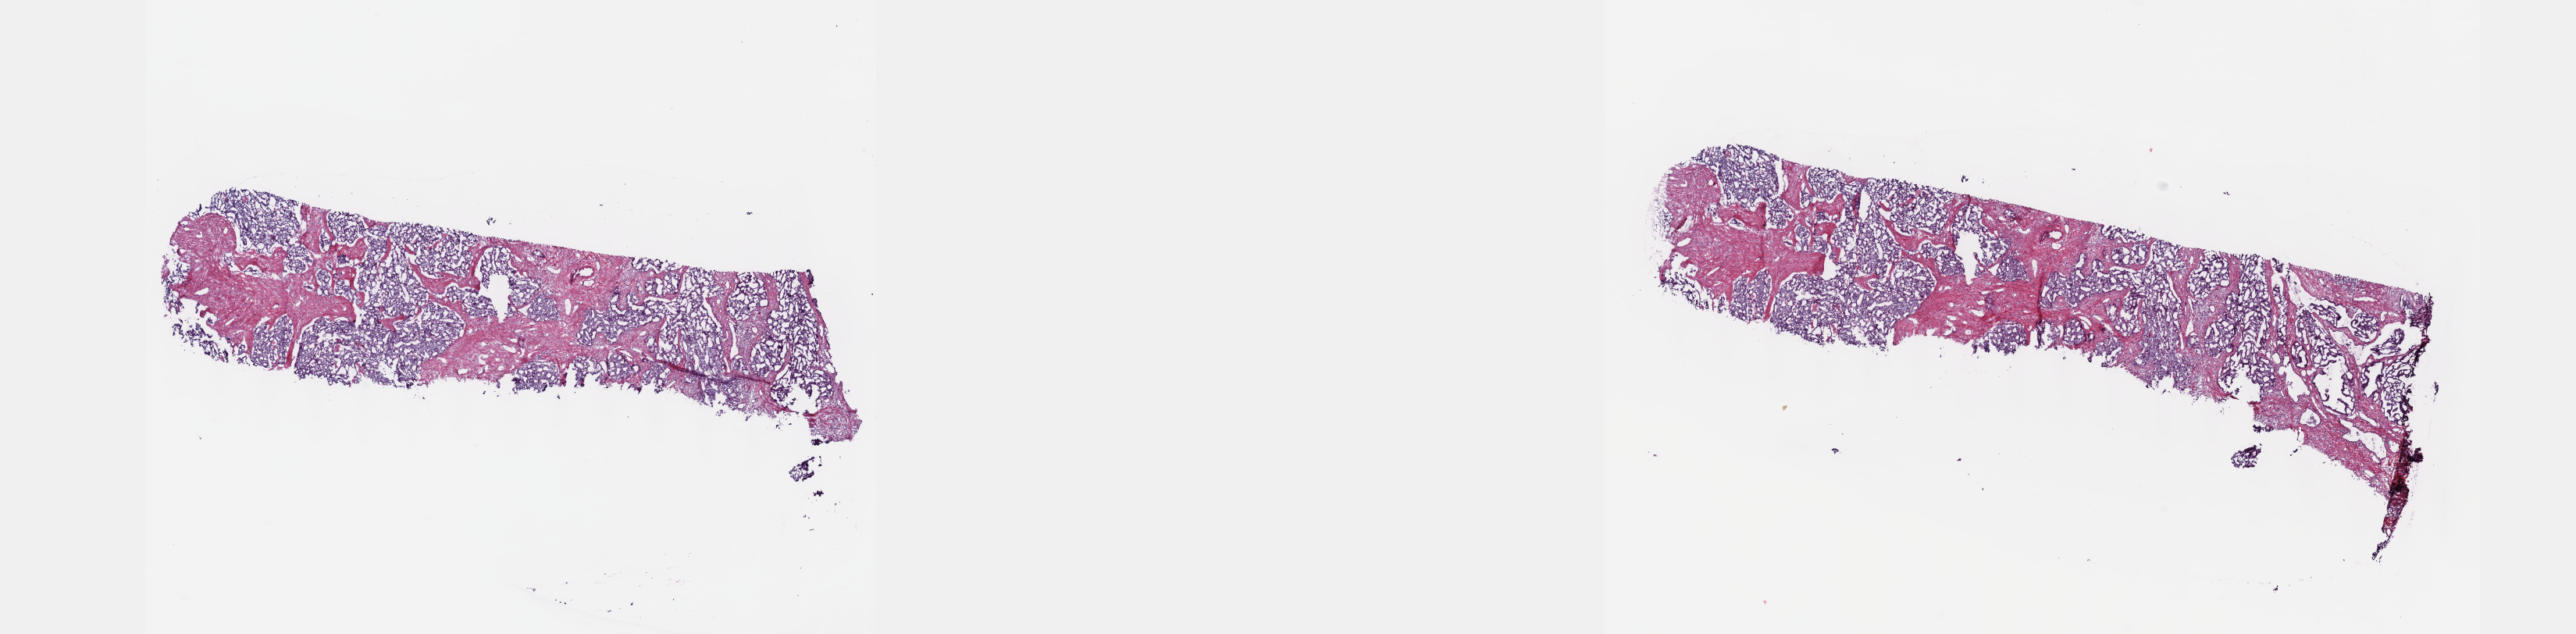
Whole-slide histology image, Hematoxylin and eosin (H&E) stained, a low-resolution overview of the entire scanned area, about 26.7 x 6.6 mm, frozen section, sample: primary tumour, prostate. Male, age 74 years at initial diagnosis.
Pathologic diagnosis: Adenocarcinoma, NOS (prostate gland).